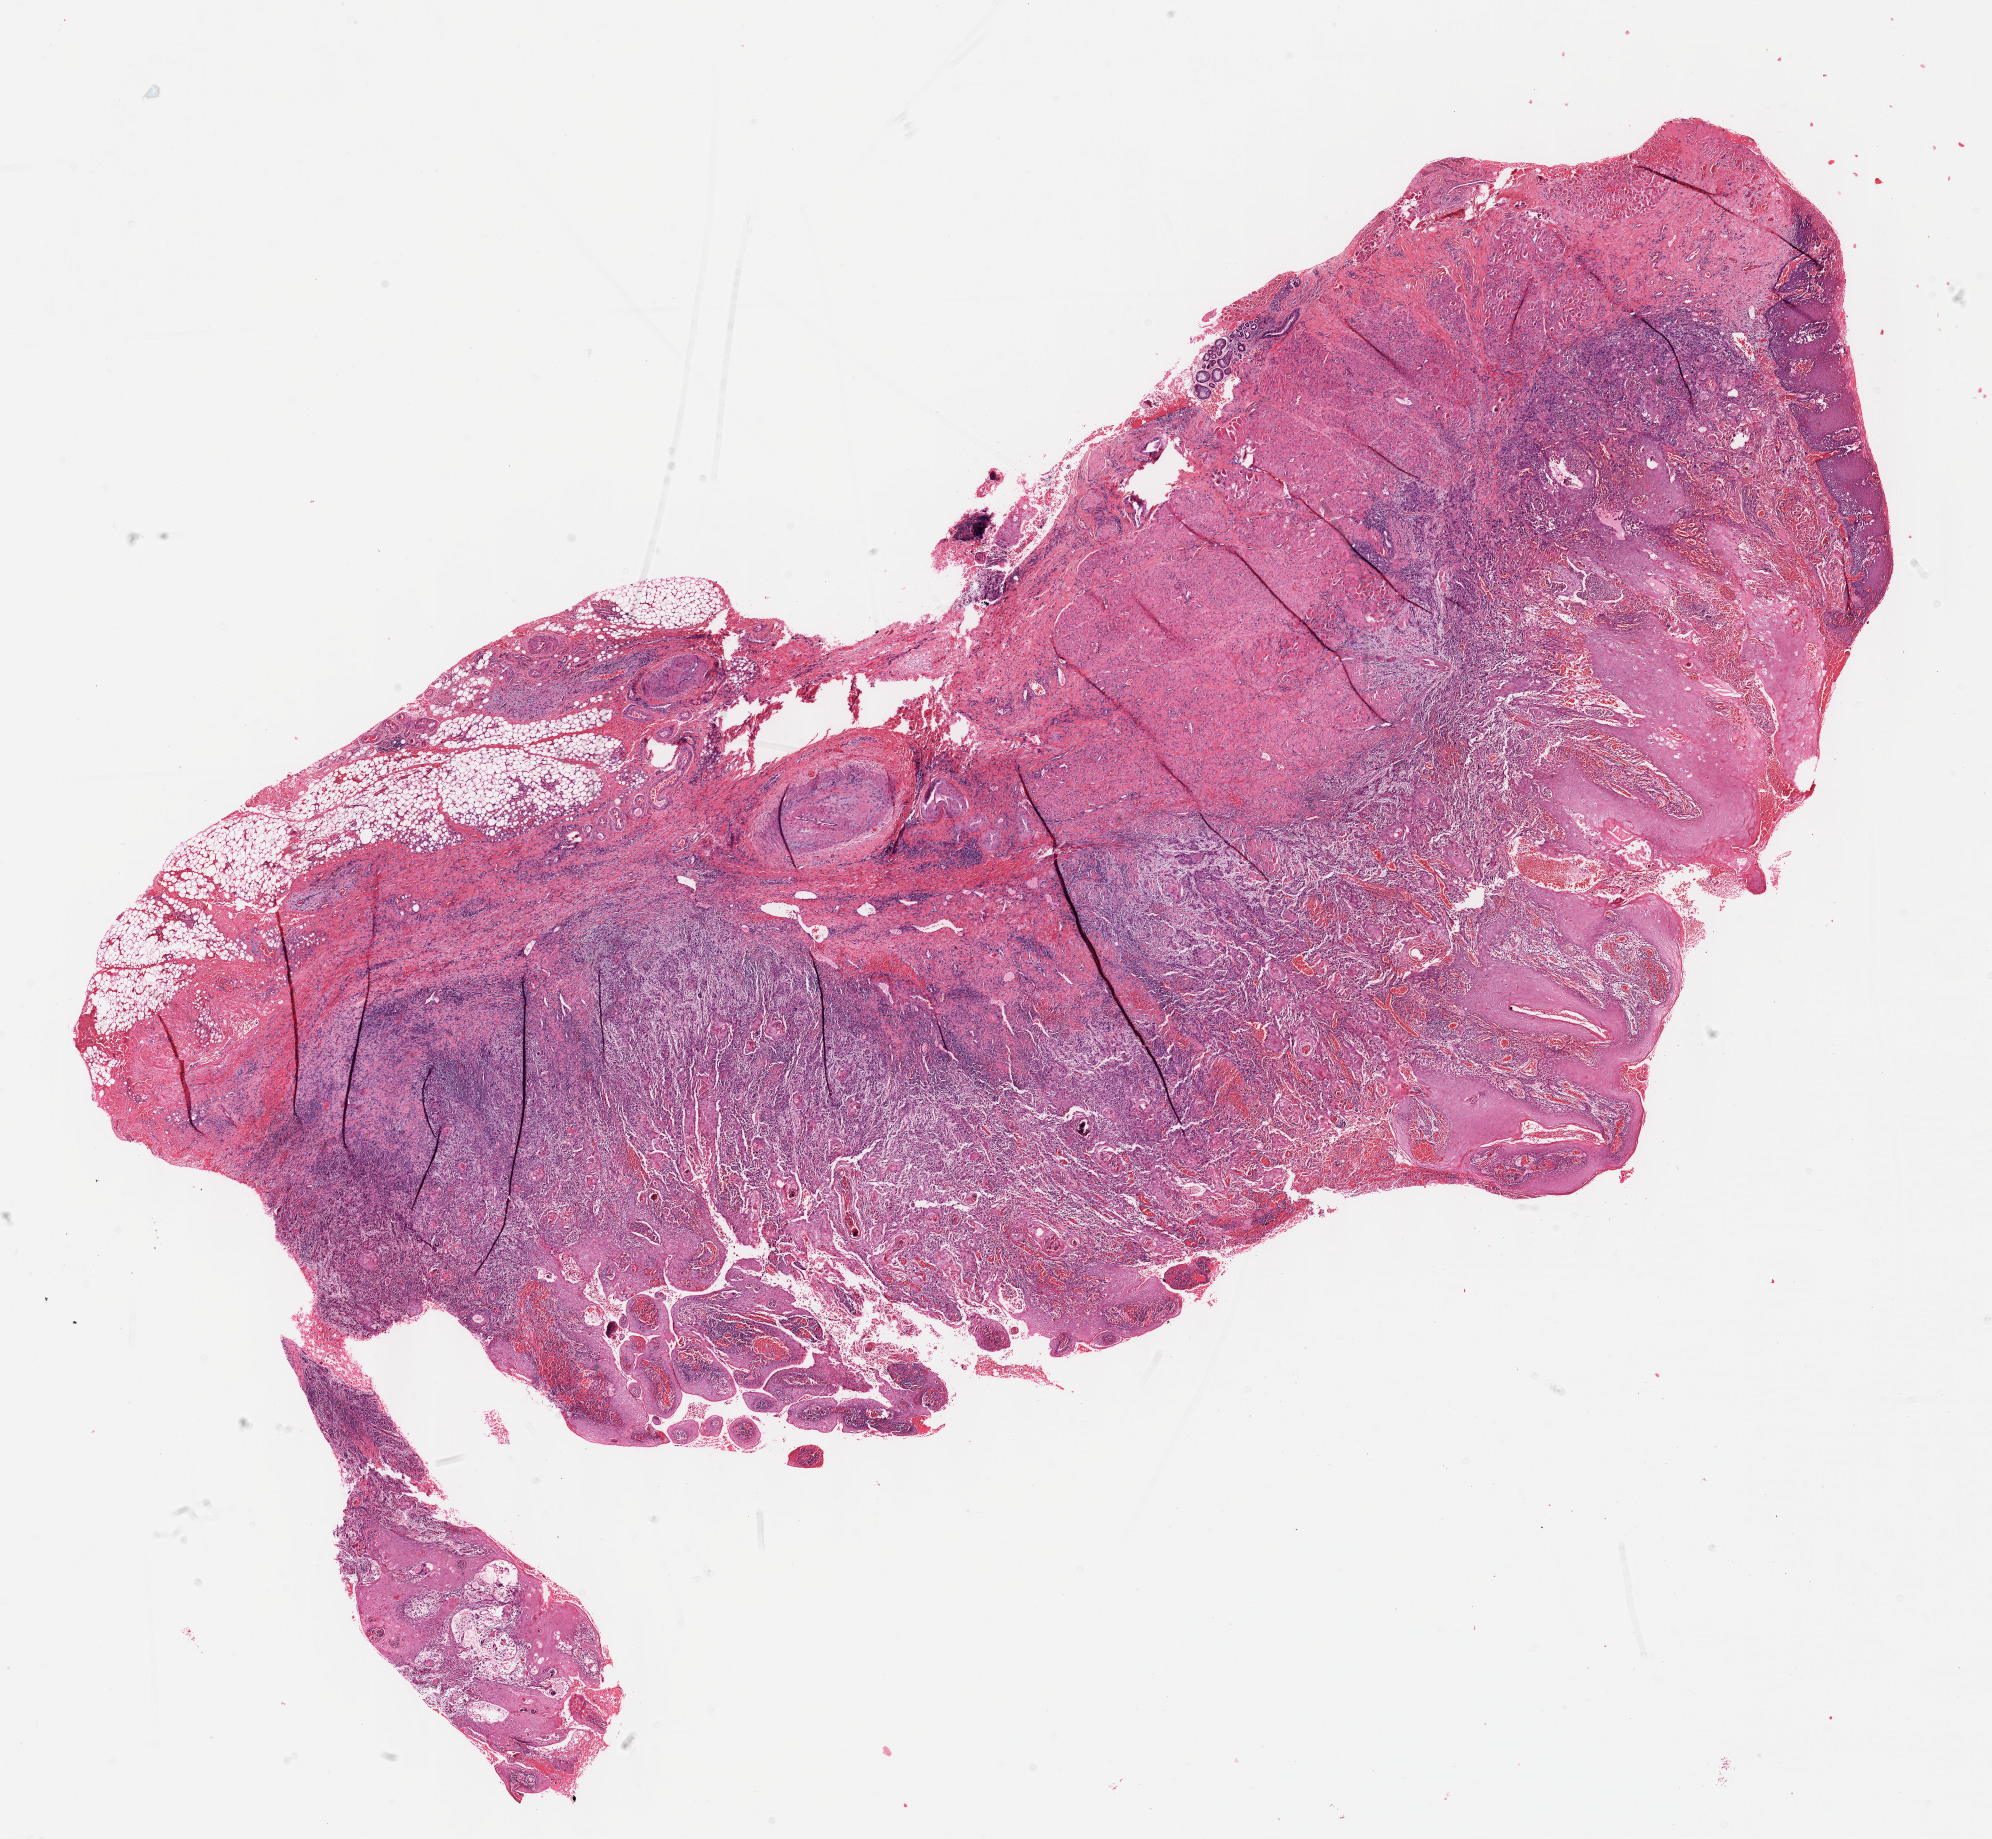
Digitized H&E tissue section (whole slide) — low-resolution overview of the scanned area, about 16.1 x 14.9 mm (from a 40x scan). FFPE section. Head and neck, primary tumour sample. Female, age 74 years at initial diagnosis. Histologic grade: G3 (poorly differentiated).
• AJCC pathologic stage: II (7th edition)
• TNM: T2 NX
• histologic diagnosis: Squamous cell carcinoma, NOS